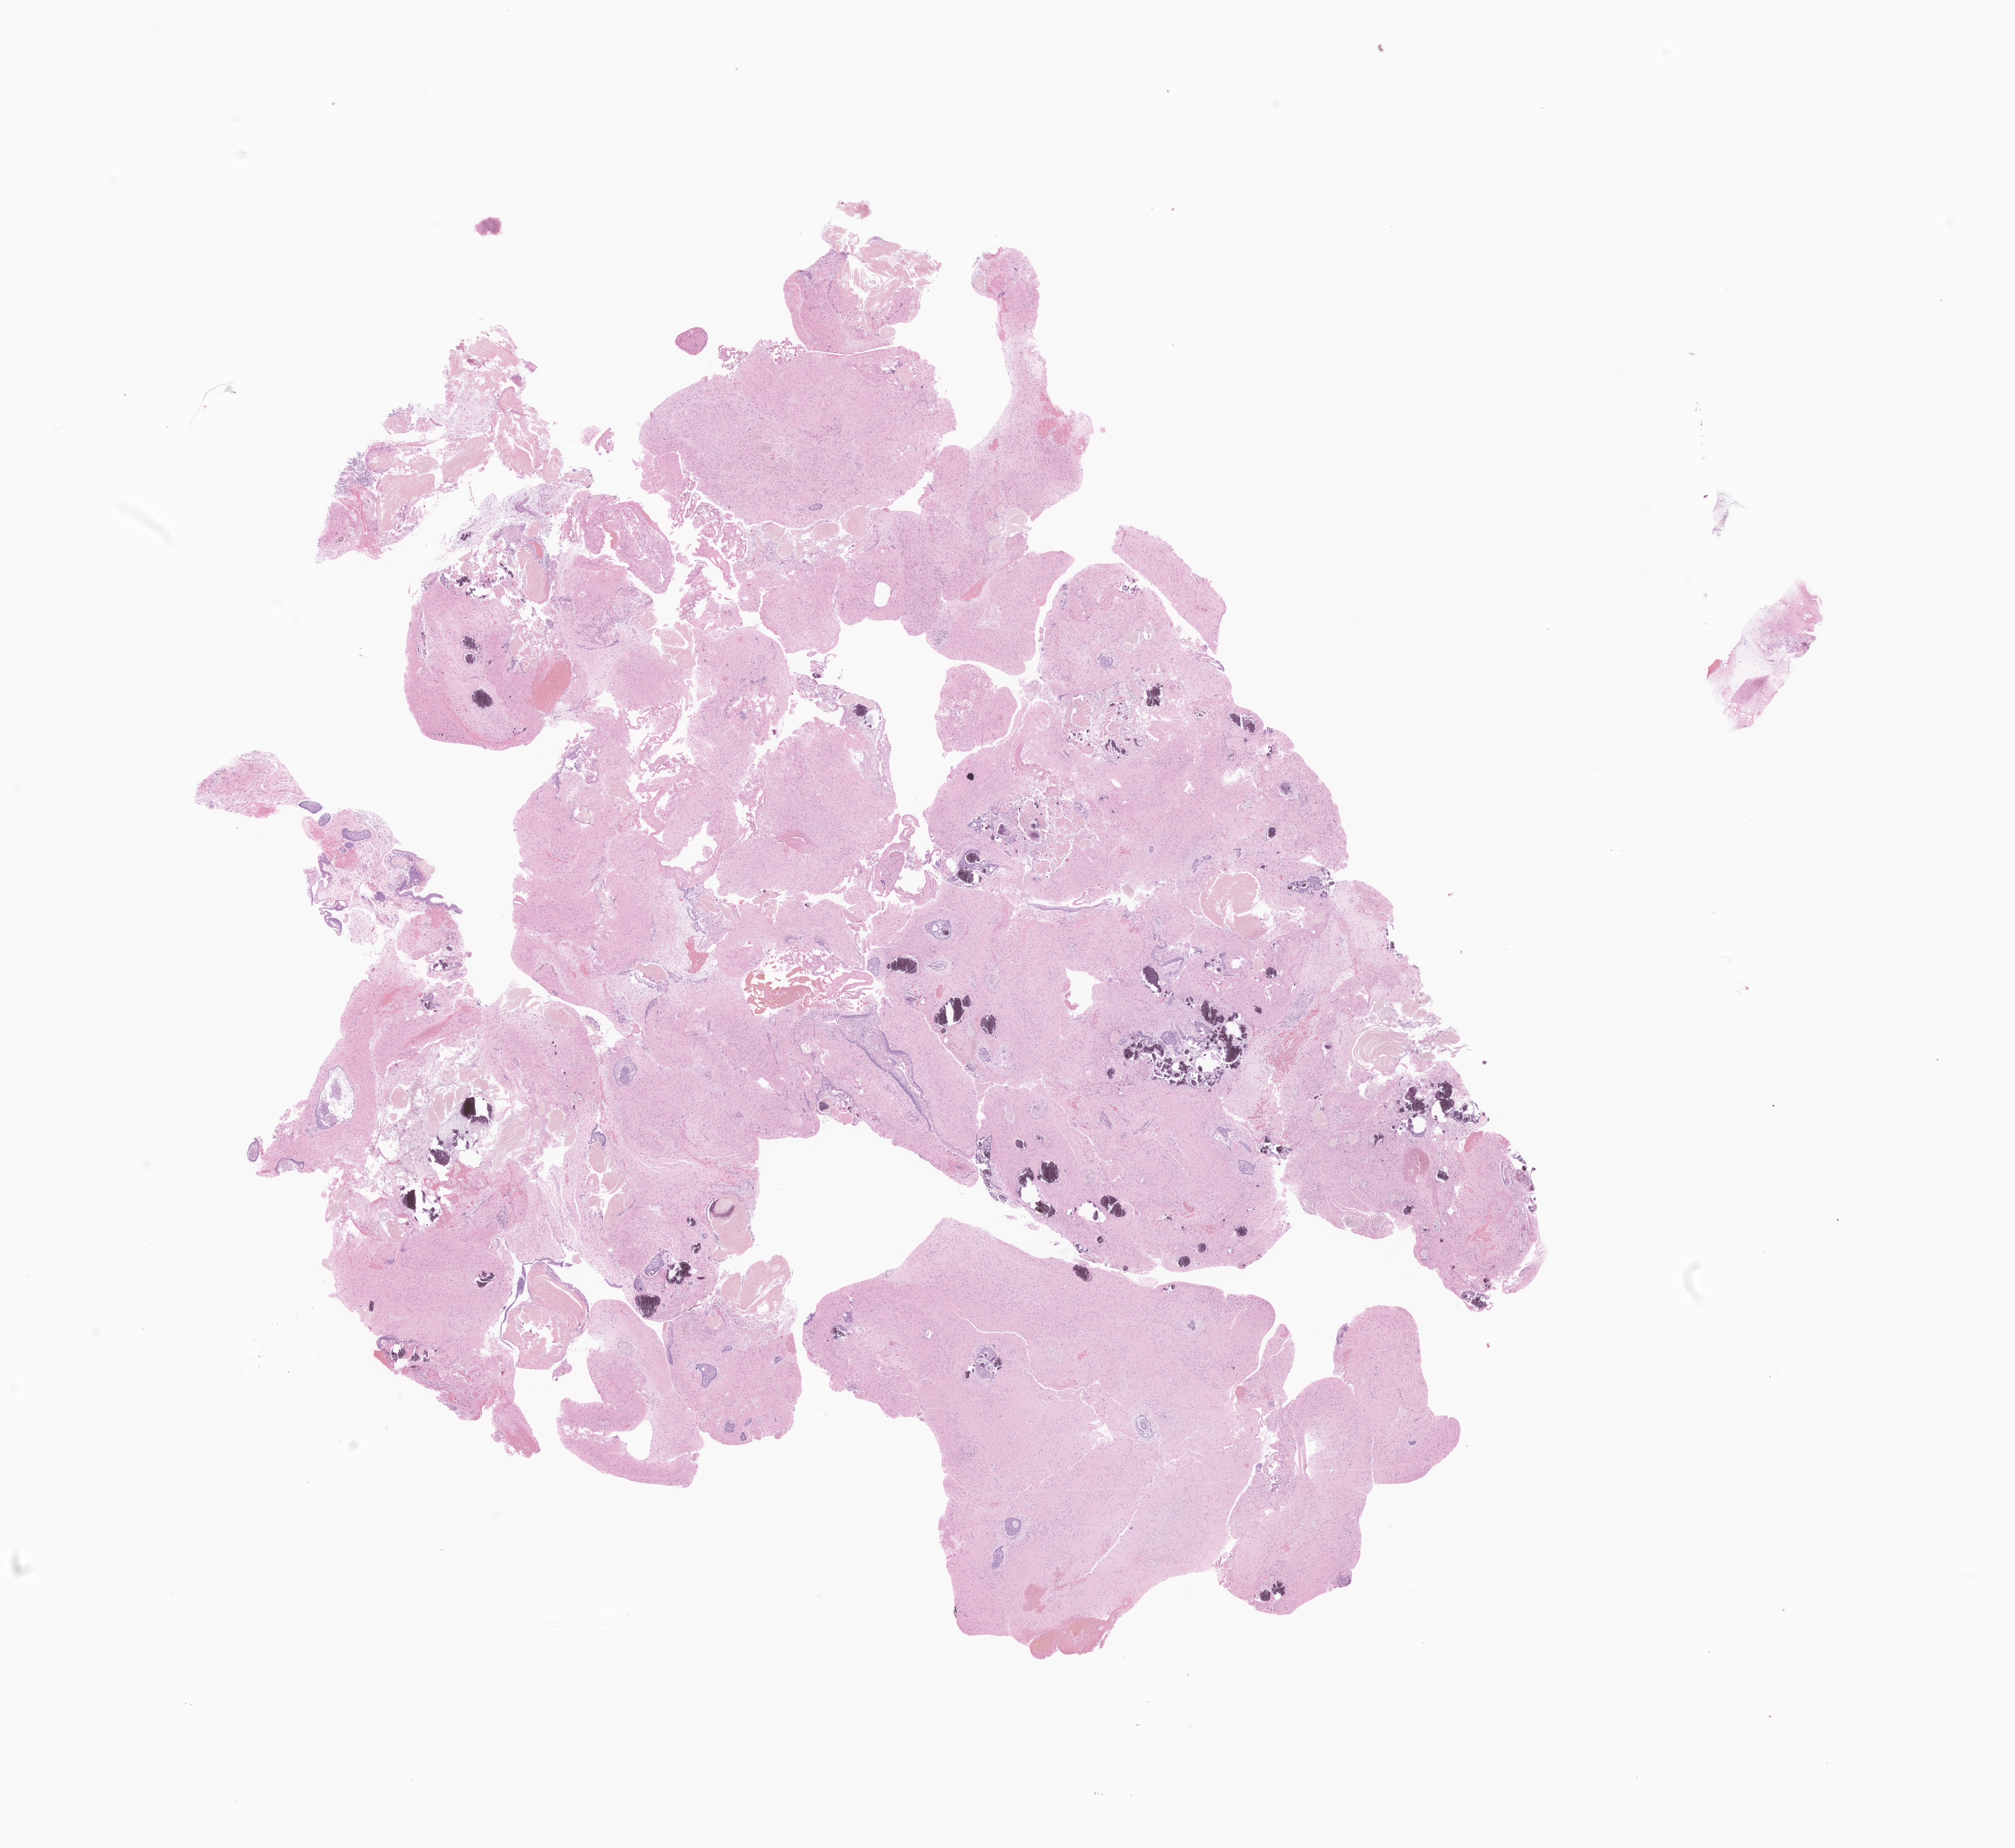
Hematoxylin and eosin (H&E) whole-slide image of tumor tissue from the brain — whole scanned area (about 19.1 x 17.6 mm) shown as a low-resolution overview; formalin-fixed paraffin-embedded section. Female patient, age 126 months (10 years 6 months).
Diagnosis: Craniopharyngioma, NOS.